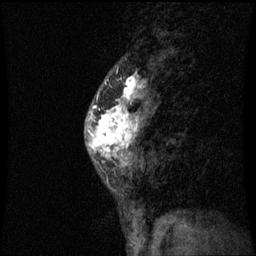
Breast MRI (dynamic contrast-enhanced), one sagittal slice. Position 26 of 60 along the scan axis. Dynamic contrast-enhanced series, image 2 of 3 at this slice position (ordered by acquisition). 1.5 T. TE 4.2 ms, TR 8.9 ms. 2 mm slice thickness. 256 × 256 image matrix, field of view 200 × 200 mm. Female patient, age 50 years. From the clinical record (not read from this slice): setting: breast cancer imaged before/during neoadjuvant chemotherapy; receptor status: triple-negative.
Outlined on this slice (semi-automatic segmentation, software-assisted and operator-edited):
- analysis volume of interest (the breast-tissue region the enhancement analysis was run in; not a lesion): bounding box (x1, y1, x2, y2) in pixels: (84, 80, 151, 171)
- tumour enhancement mask (voxels above the 70 % enhancement threshold inside the analysis volume of interest): (88, 80, 143, 165)